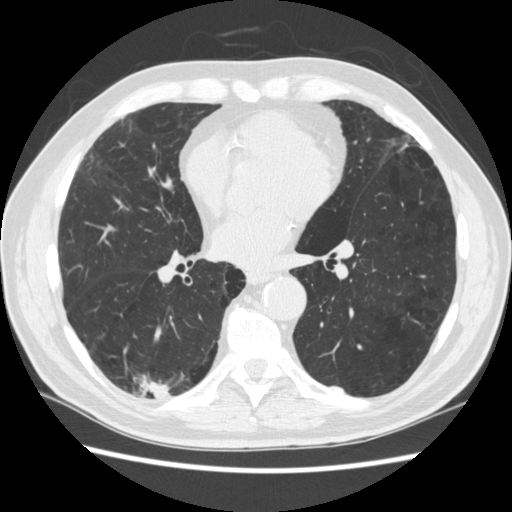
Low-dose screening chest CT, axial slice, third screening round (two years after baseline), lung window (W 1500 / L -600 HU), 120 kVp, 512 × 512 image matrix. Male, age 70 years at enrolment. Former smoker at enrolment.
- Expert reader's lesion annotation, bounding box [x1, y1, x2, y2] px = [122, 361, 184, 420].
- The screening reader recorded 4 non-calcified nodules or masses ≥4 mm on this exam (right lower lobe, right lower lobe, left lower lobe, left lower lobe); which of them this box marks is not recorded.
- Official screen result: positive, other.
- Lung cancer was diagnosed 253 days after this screen: squamous cell carcinoma, NOS, right upper lobe, poorly differentiated (G3), stage IV (AJCC 6th edition).